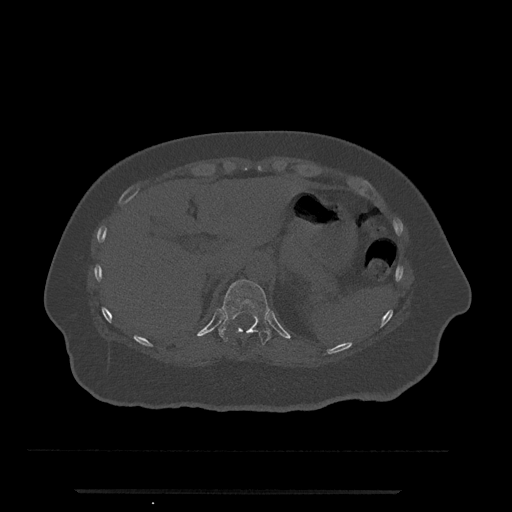
CT including the spine, one axial slice. Position 237 of 797 along the scan axis. Reconstruction kernel Br40s/3. Bone window (W 1800 / L 400 HU). 0.5 mm slice thickness. 512 × 512 image matrix, field of view 440 × 440 mm. Female patient, age 51 years. From the clinical record (not read from this slice): primary cancer: neuro; vertebrae with lytic lesions (as recorded): T8.
Annotated regions visible in this slice (semi-automatic segmentation, software-assisted and operator-edited):
- T11 vertebra: bounding box <218,279,271,346> (left, top, right, bottom; pixels)